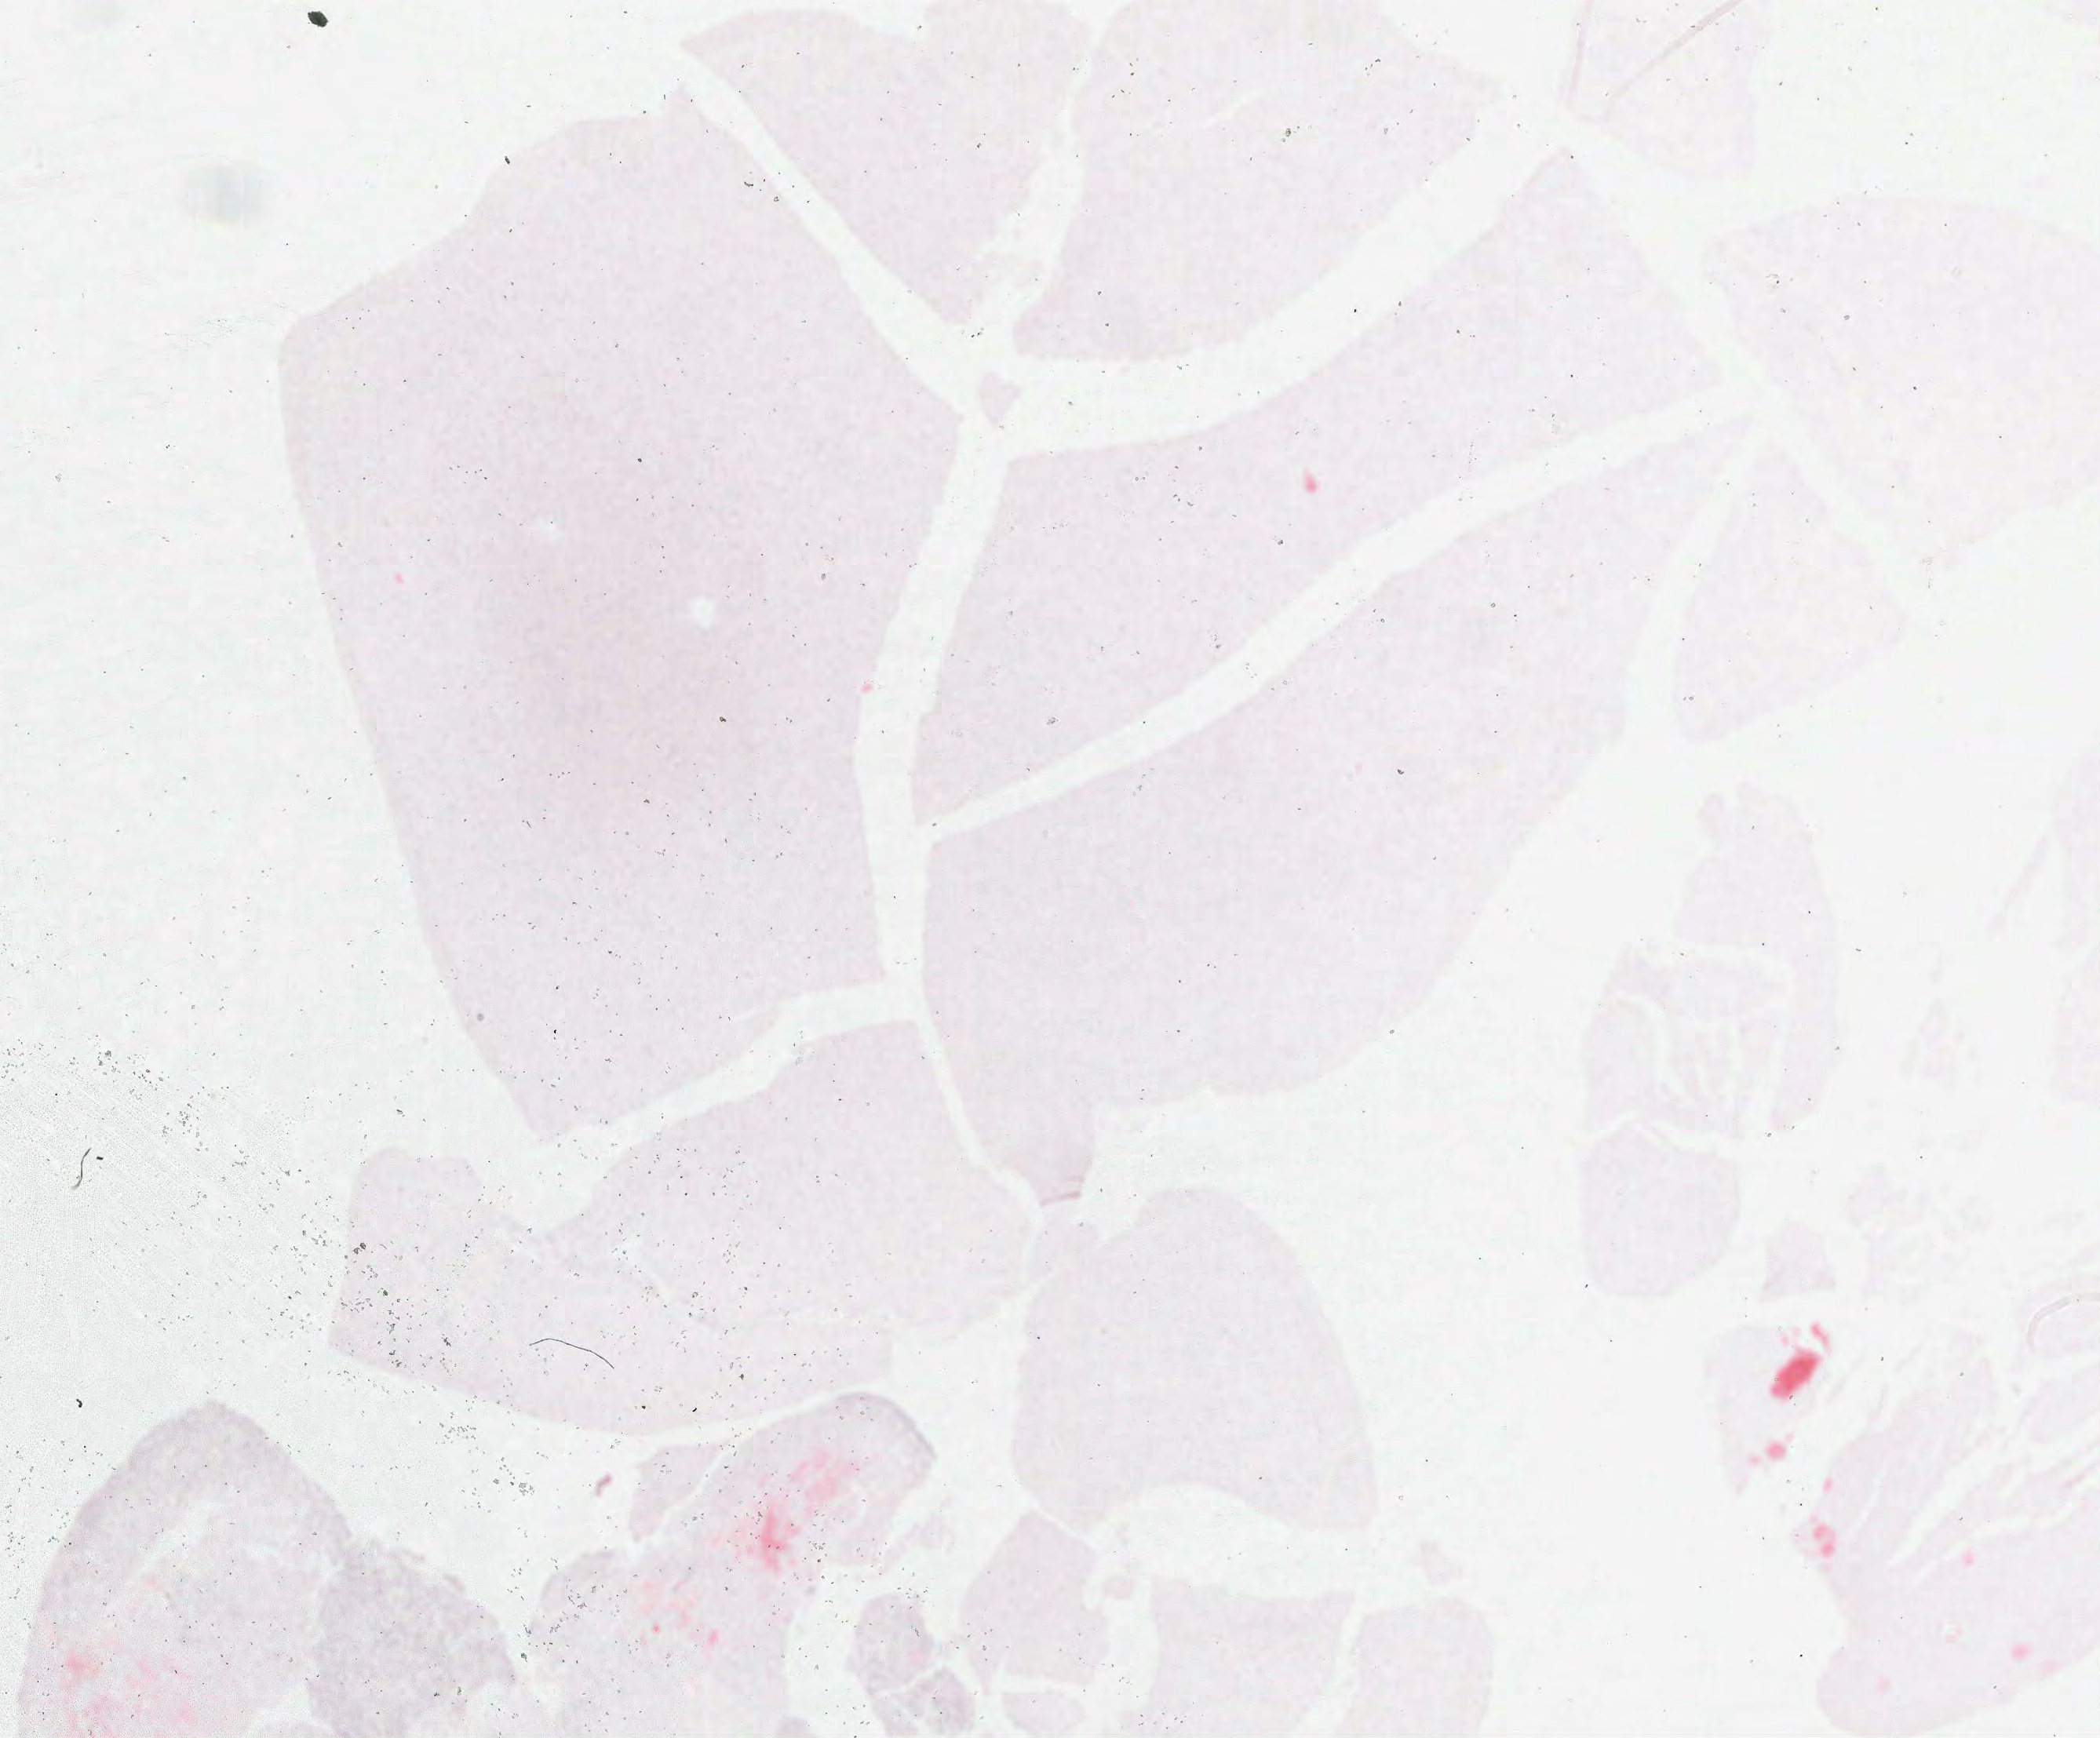
Digitized H&E tissue section (whole slide) — a low-resolution overview of the entire scanned area, about 21.0 x 17.4 mm (from a 40x scan). FFPE section. Sample: primary tumour, brain. Male patient; age at initial diagnosis 61 years.
Pathologic diagnosis: Glioblastoma.